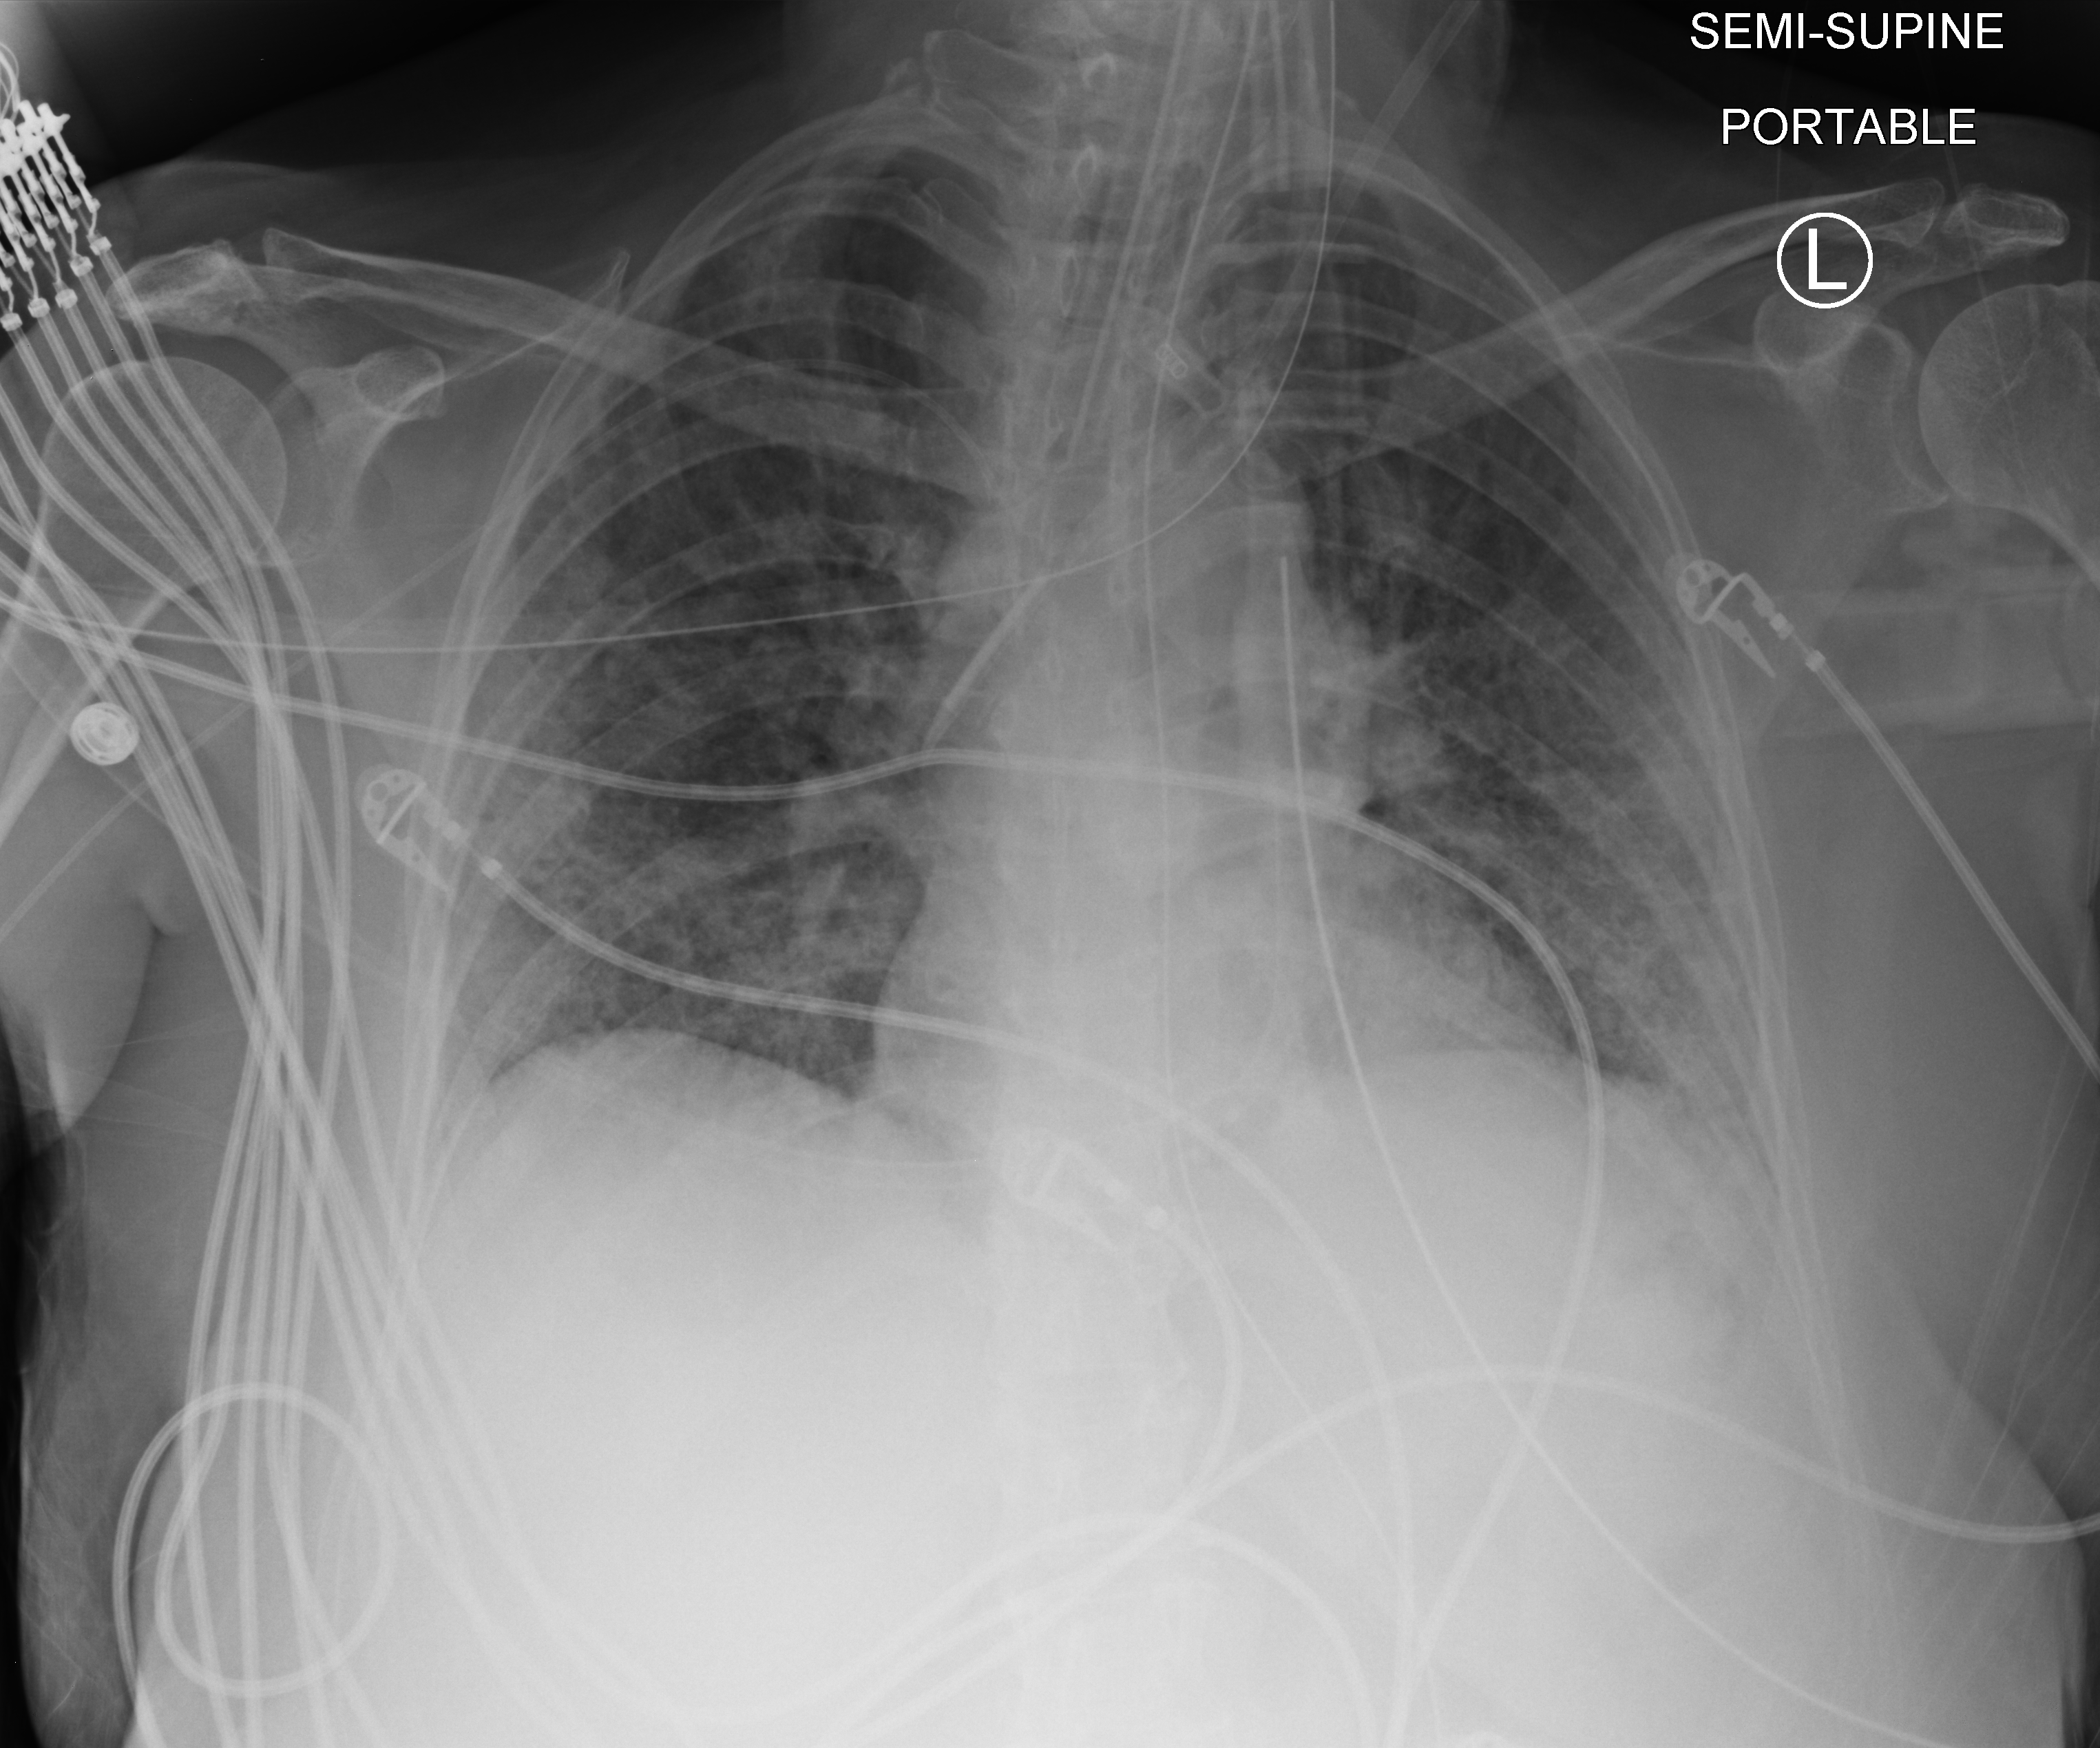
Chest X-ray (portable); anteroposterior (AP) projection. Female patient hospitalised with COVID-19, age 60–74 years.
From the hospital-stay record, not from the radiograph (when in the stay this image was taken is not recorded):
- admitted to intensive care during this hospital stay: yes
- mechanically ventilated during this hospital stay: yes
- other chronic lung disease (admission record): no